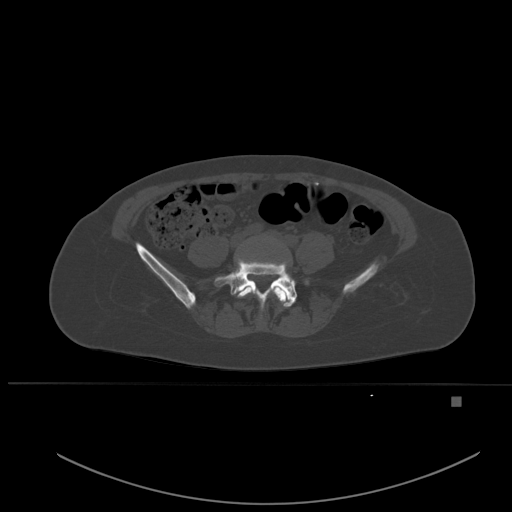
CT including the spine, one axial slice; slice 160 of 651 in the series (ordered by position); bone window (W 1800 / L 400 HU); 1.5 mm slice thickness; 512 × 512 image matrix, field of view 443 × 443 mm. Female patient, age 49 years. Case-level facts recorded for this patient, not image findings: primary cancer: breast; vertebrae with lytic lesions (as recorded): L3, T12, L4.
Structures marked on this image (semi-automatically segmented with operator editing):
- L4 vertebra: bounding box [x1, y1, x2, y2] px = [237, 281, 288, 303]
- L5 vertebra: [214, 258, 297, 307]